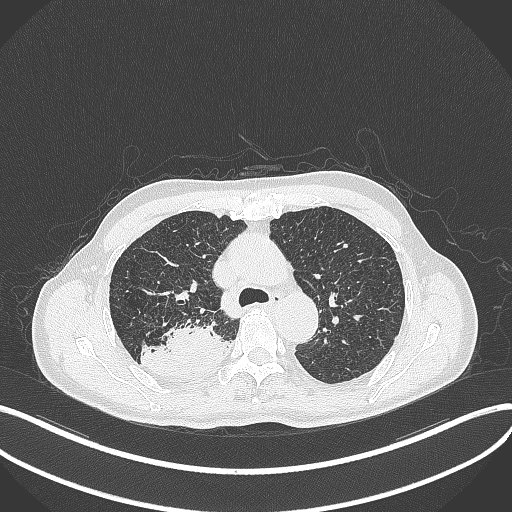
Chest CT, one axial slice. Slice 318 of 428 in the series (ordered by position). Reconstruction kernel B70f. 120 kVp. Lung window (W 1500 / L -600 HU). 1 mm slice thickness. 512 × 512 image matrix, field of view 400 × 400 mm. Patient: male, 79 years. Case-level facts recorded for this patient, not image findings: clinical TNM (as recorded): T3 N0 M0.
Structures marked on this image (bounding box drawn by a radiologist):
- lung tumour (recorded histology: adenocarcinoma): bounding box [x1, y1, x2, y2] px = [140, 317, 229, 381]